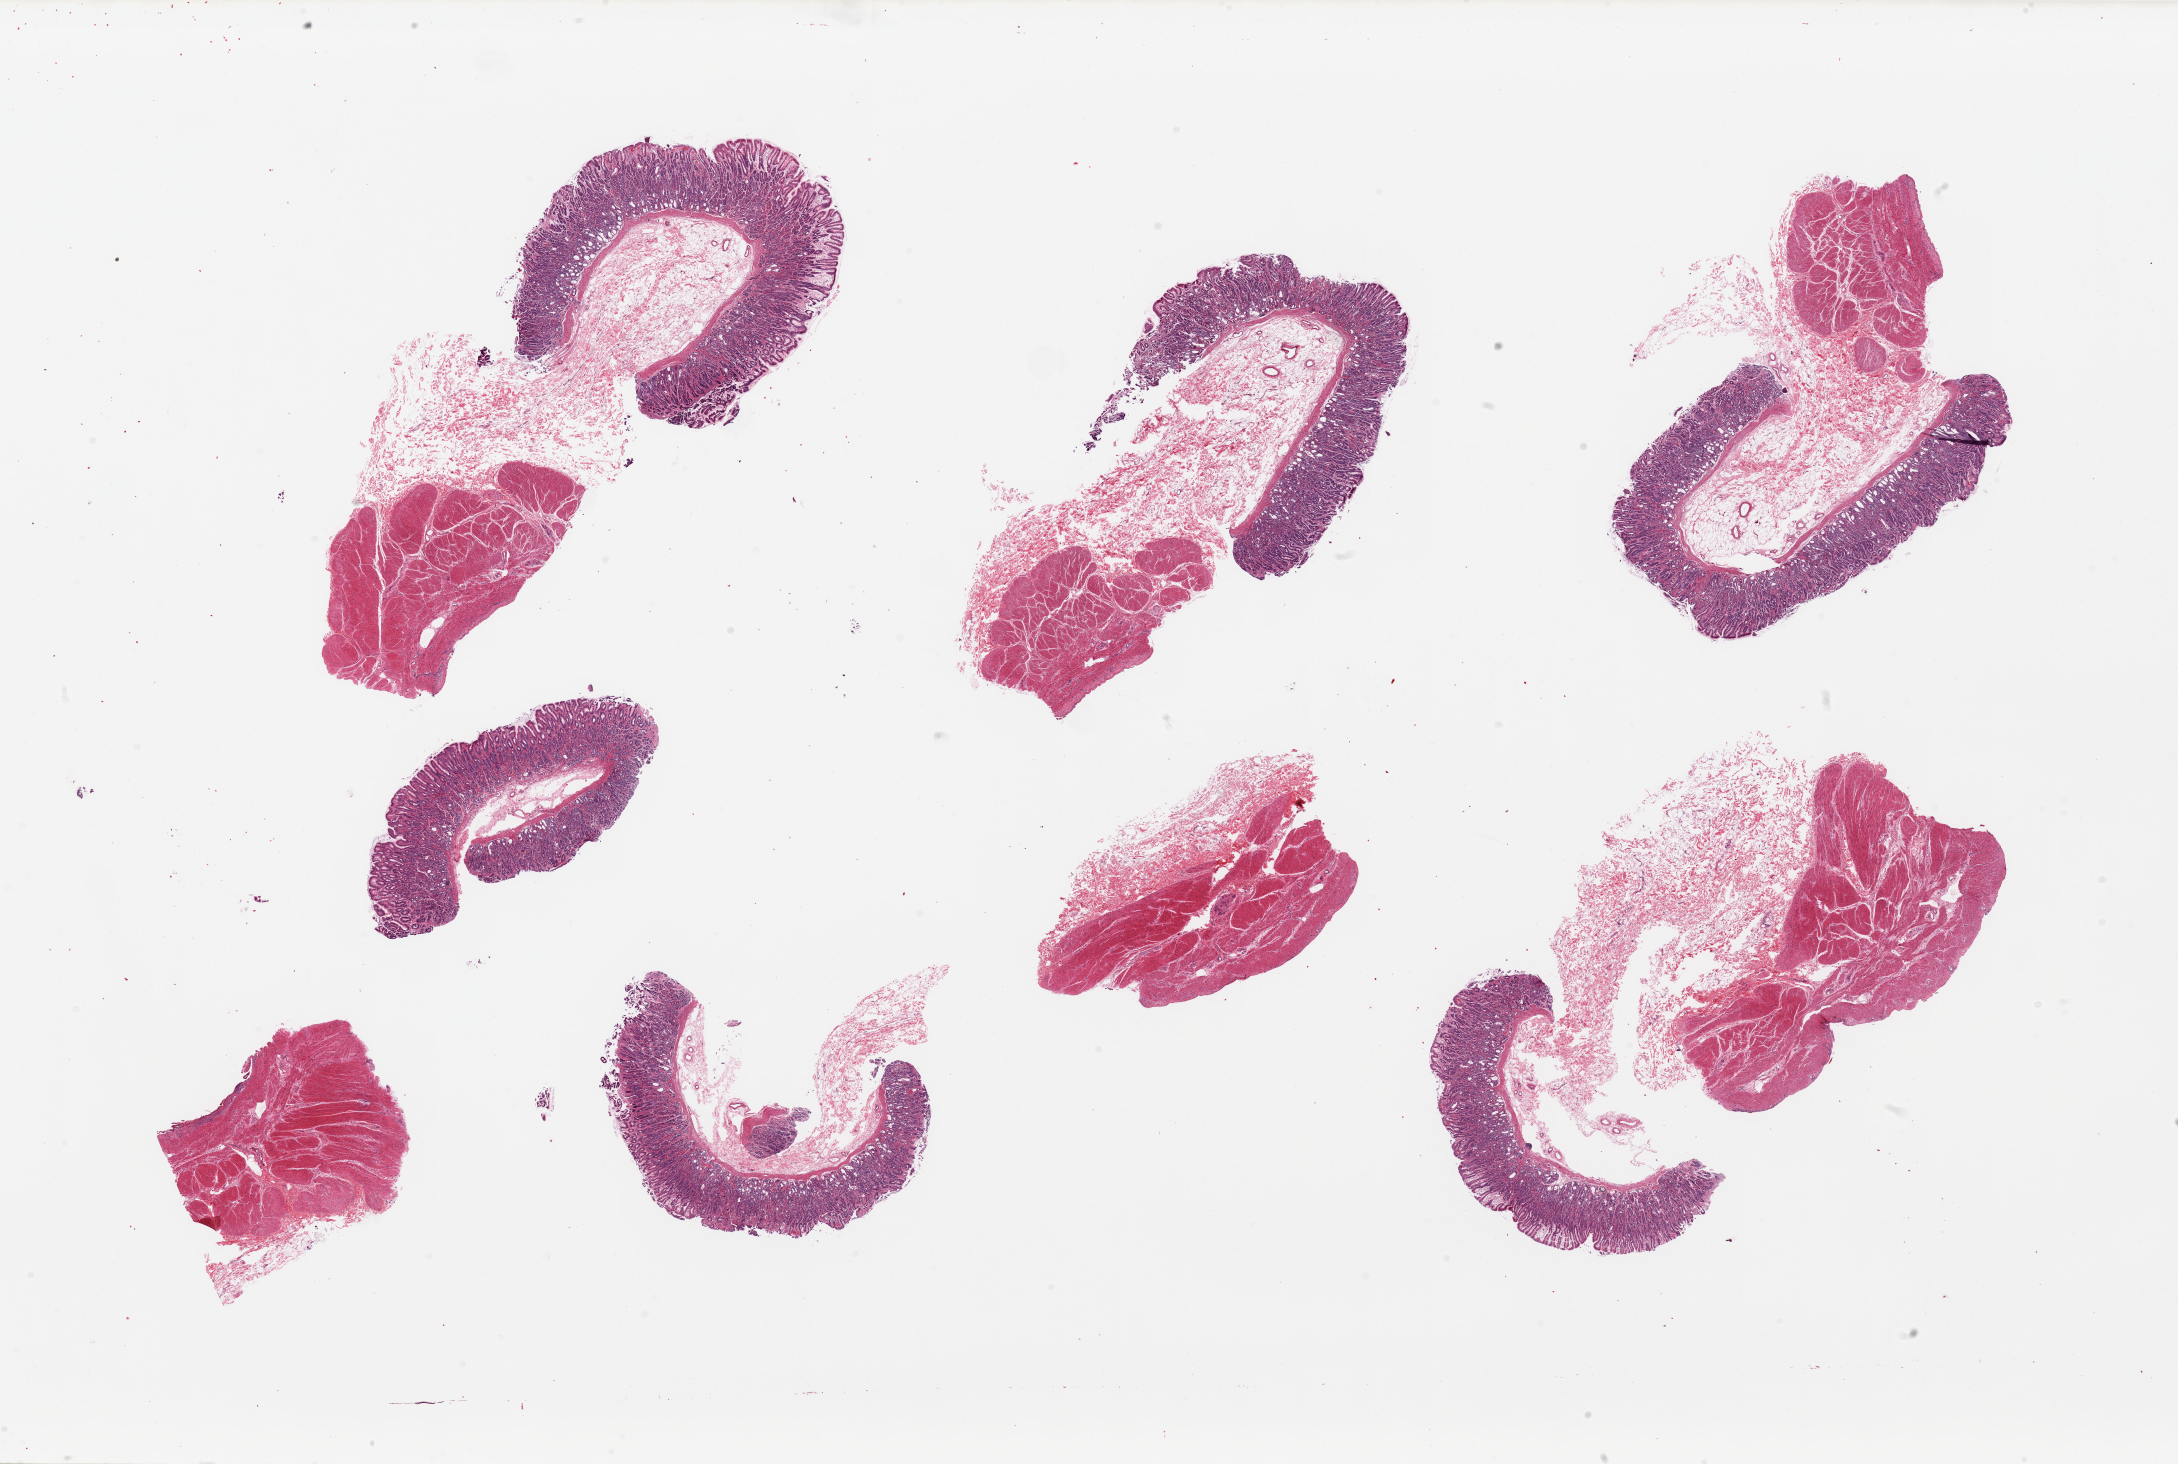
Digitized haematoxylin and eosin-stained section — shown as a low-resolution overview of the whole scanned area (about 34.5 x 23.2 mm, from a 20x scan). PAXgene-fixed paraffin-embedded (PFPE) section. Target tissue: stomach. Donor tissue sample. Donor: female.
• review note (as recorded): 8 pieces, mucosa and muscularis, acute gastritis